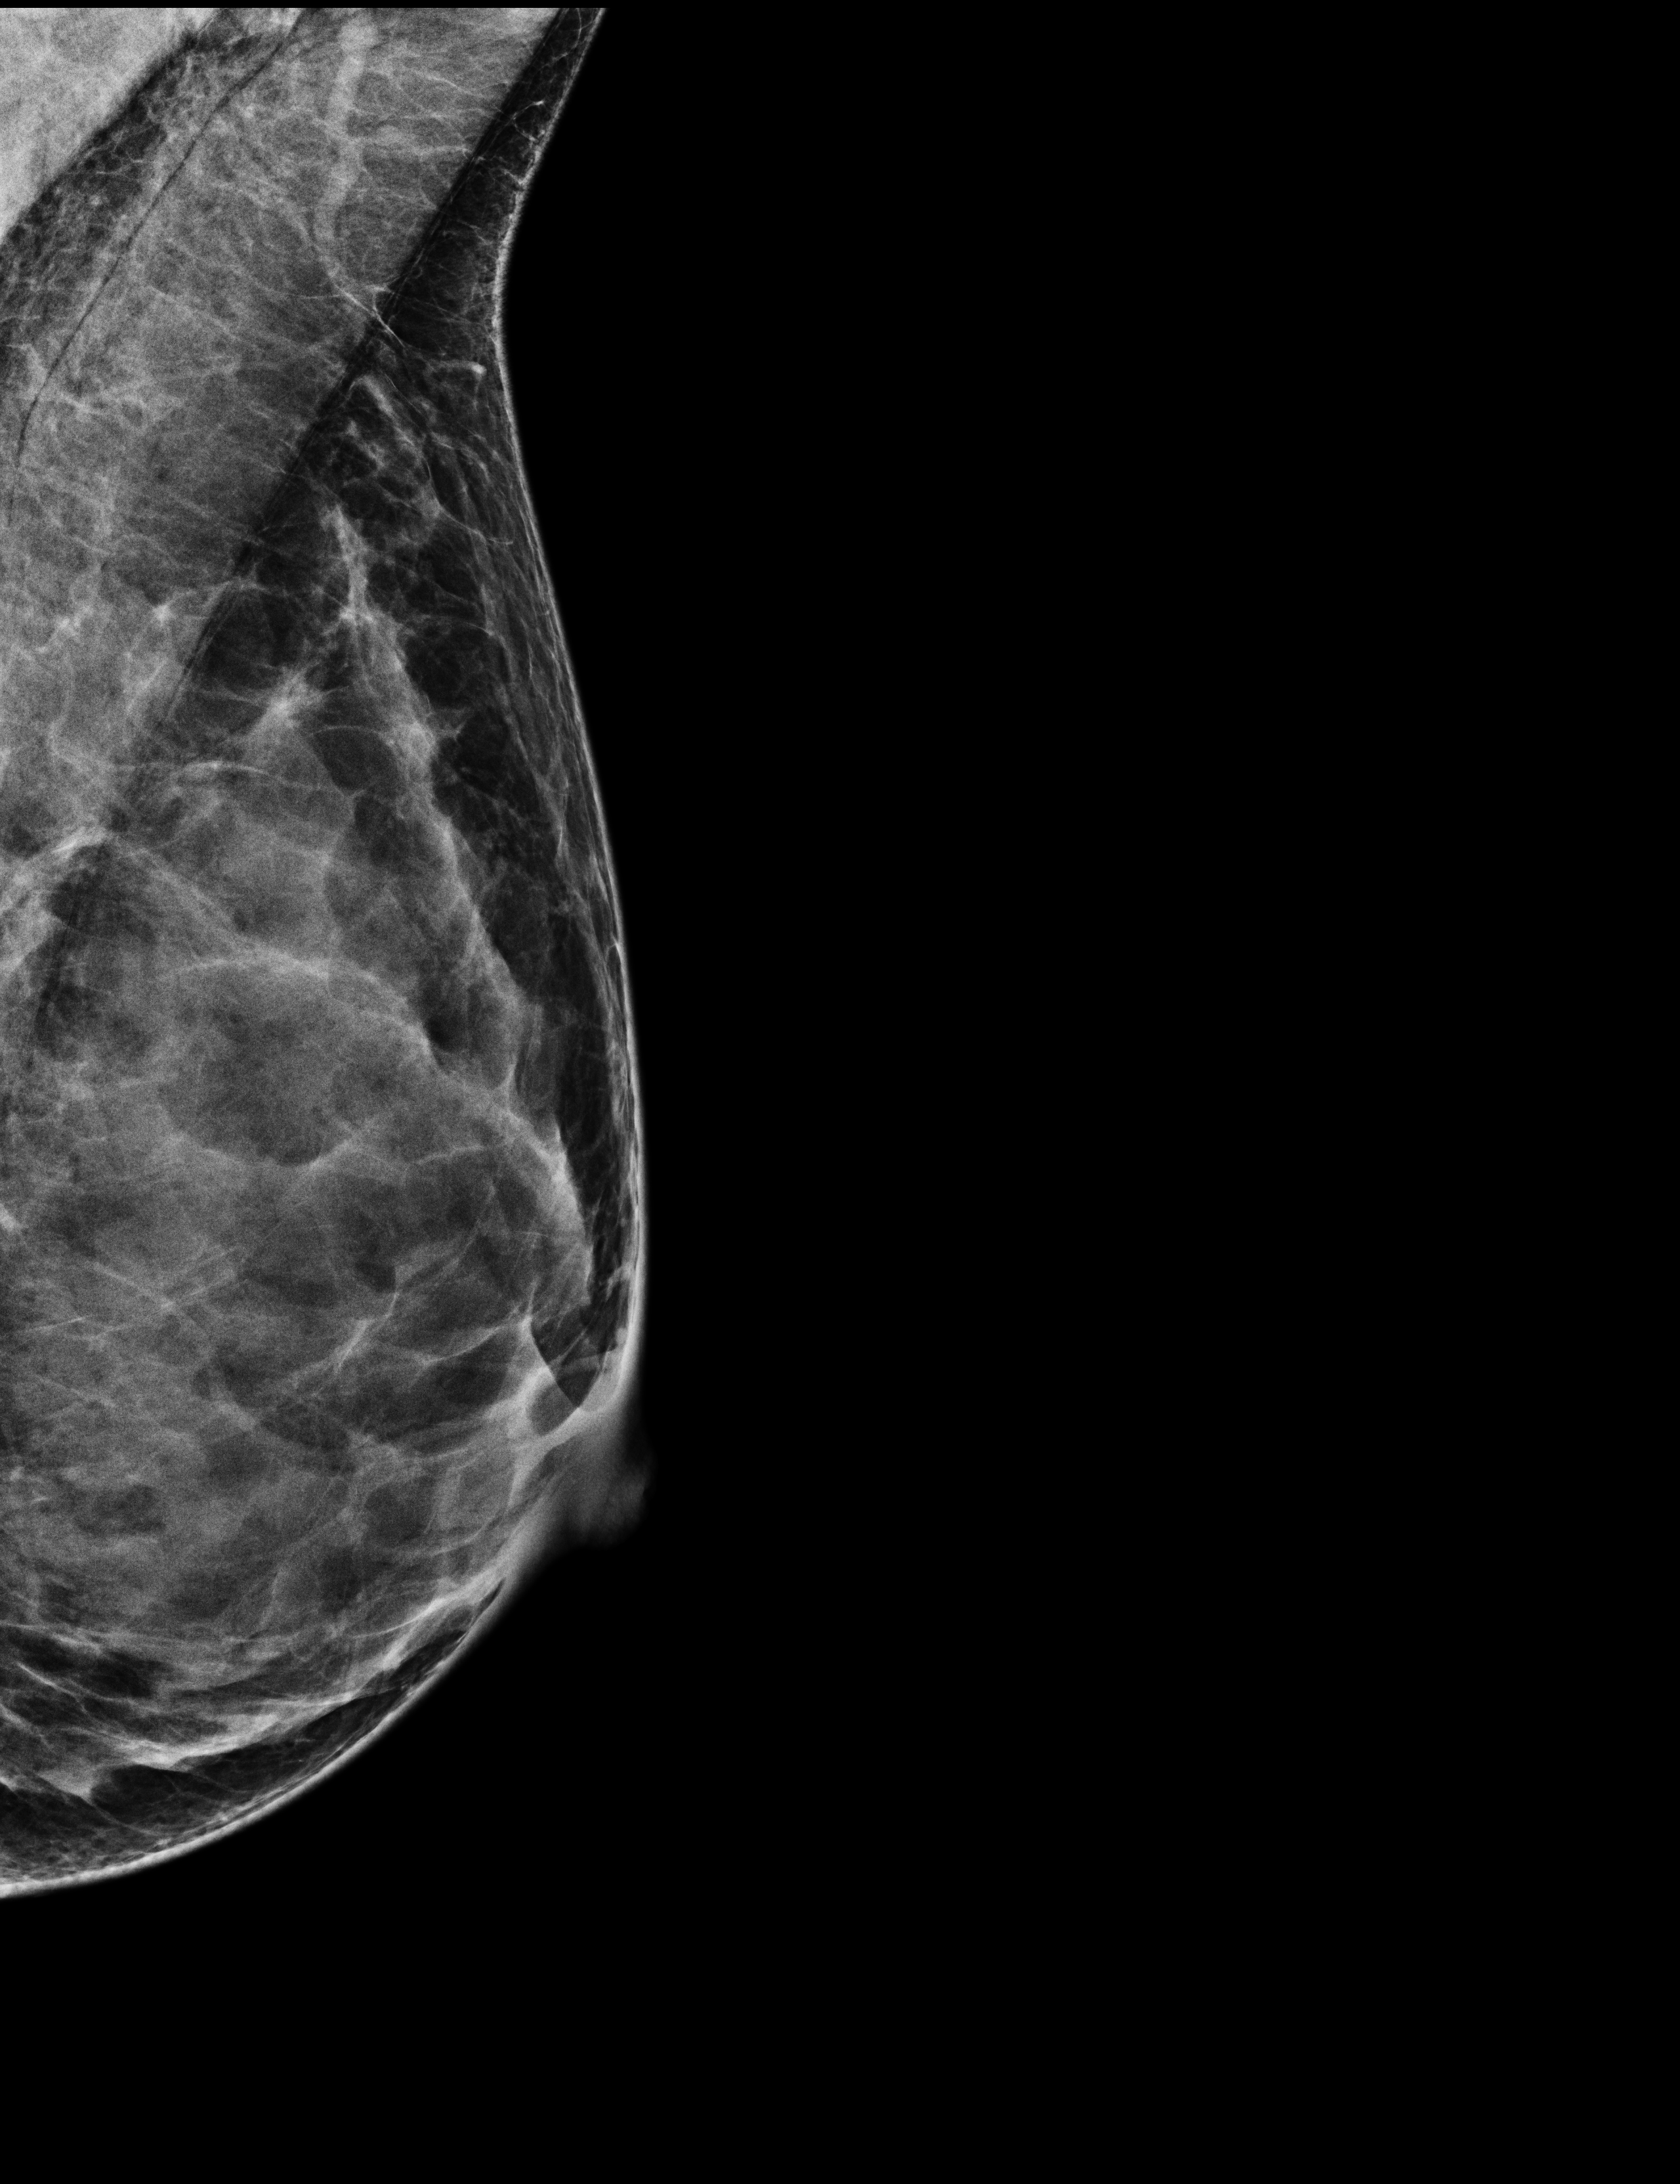
Full-field digital mammogram (FFDM), left breast, MLO view, screening examination, compressed breast thickness 38 mm, system: Selenia Dimensions. Female patient, age 42 years.
BI-RADS breast density category at the screening exam (both breasts, scale 1–4): 4. Final BI-RADS assessment for this screening round (tomosynthesis exam, both breasts): category 1. Recall: no recall after this screen.